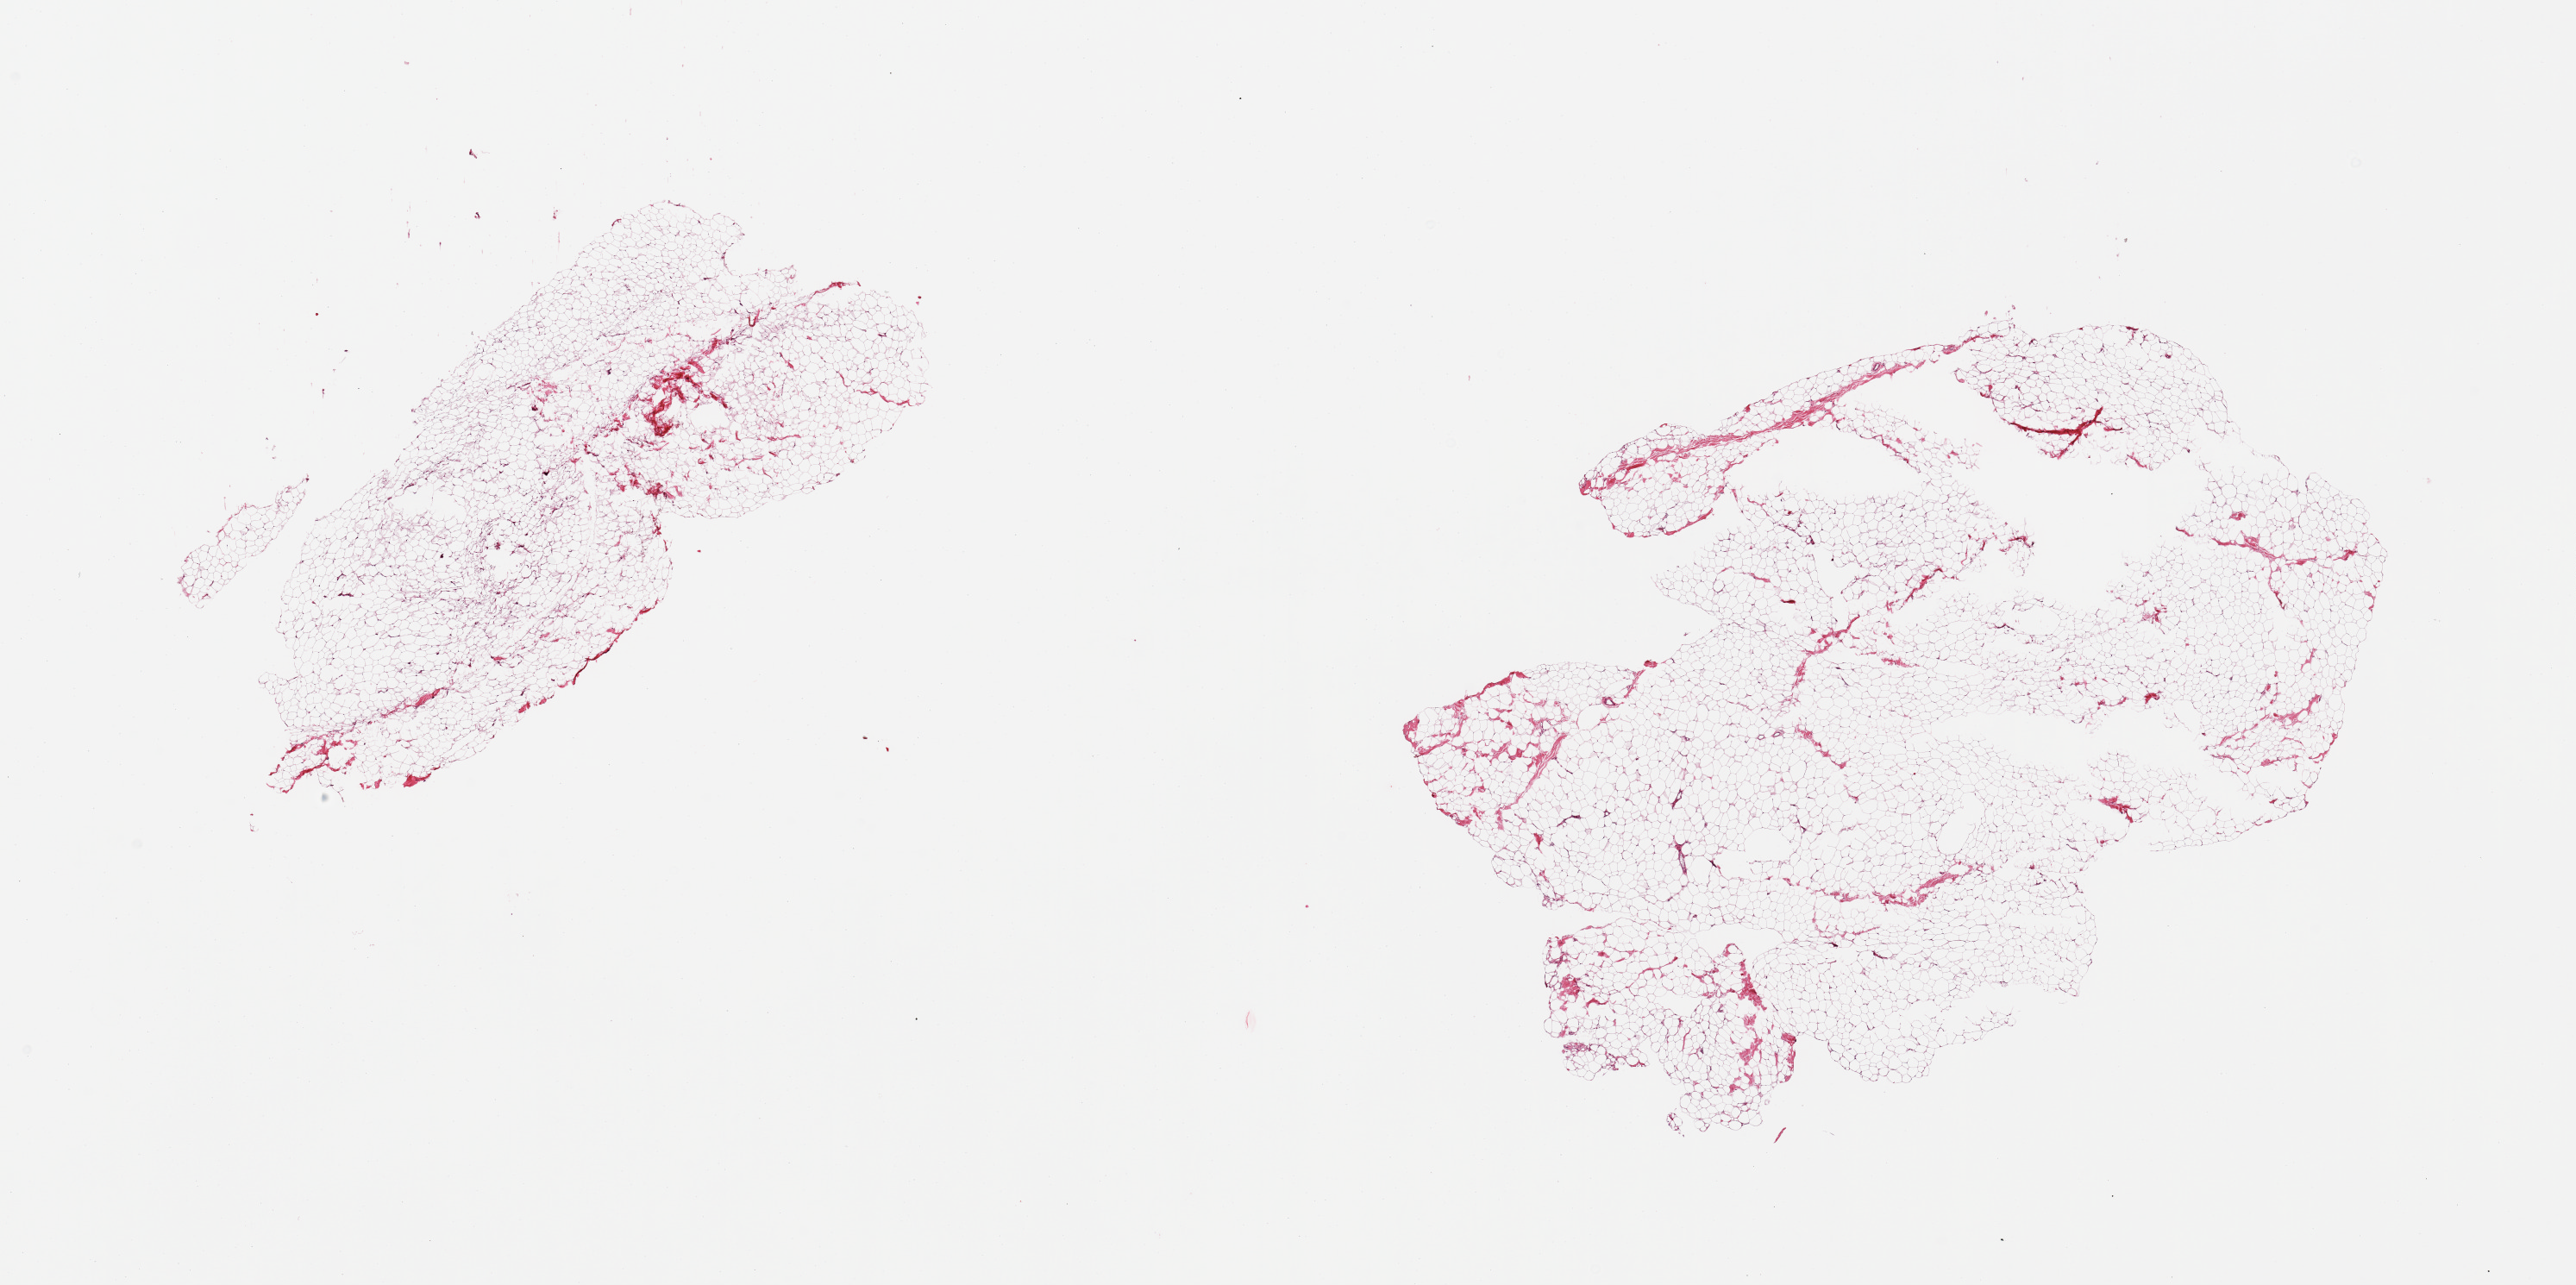
Digitized H&E-stained section, shown as a low-resolution overview of the whole scanned area (about 23.6 x 11.8 mm). PAXgene-fixed, paraffin-embedded tissue. Target tissue: breast. Donor tissue sample. Donor sex: male.
Reviewer comment on this tissue sample: 2 pieces, fibroadipose parenchymal elements, no ductal elements.